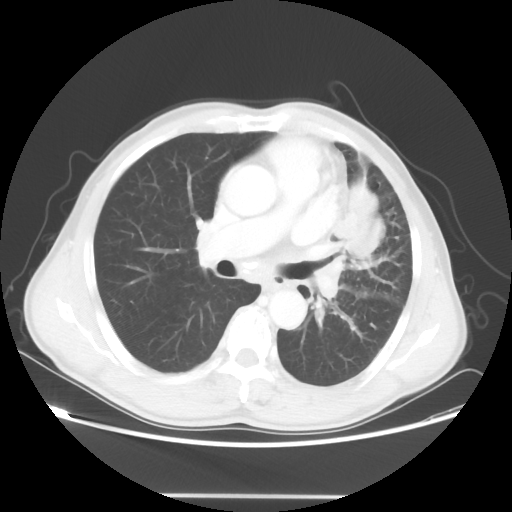
Chest CT, one axial slice; slice 29 of 55 in the series (ordered by position); reconstruction kernel STANDARD; lung window (W 1500 / L -600 HU); 5 mm slice thickness; 512 × 512 image matrix. Patient: male, 60 years. Case-level facts recorded for this patient, not image findings: clinical TNM (as recorded): T3 N3 M0.
Structures marked on this image (bounding box drawn by a radiologist):
- lung tumour (recorded histology: adenocarcinoma): bounding box <340,176,385,276> (left, top, right, bottom; pixels)